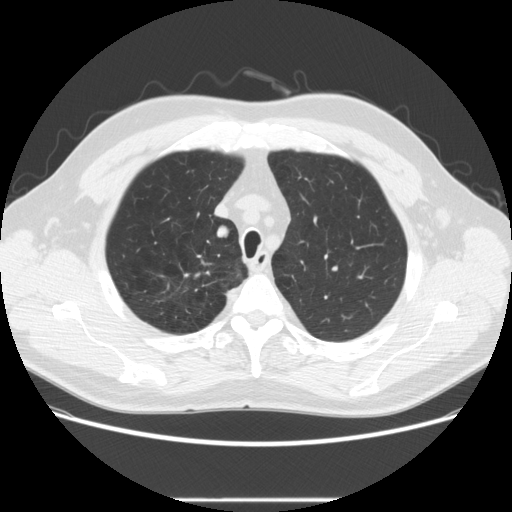
Low-dose screening chest CT, axial slice; baseline screening round; lung window (W 1500 / L -600 HU); 2.5 mm slice thickness. Male participant, aged 64 years at enrolment. Former smoker at enrolment.
Lesion marked by an expert reader, bounding box [x1, y1, x2, y2] px = [196, 220, 239, 252]. The screening reader recorded 2 non-calcified nodules or masses ≥4 mm on this exam (right upper lobe, right upper lobe); which of them this box marks is not recorded. Official screen result: positive, change unspecified: nodule(s) >= 4 mm or enlarging nodule(s), mass(es), or other non-specific abnormalities suspicious for lung cancer. Participant outcome: lung cancer diagnosed 753 days after this screen — adenocarcinoma, NOS, right upper lobe, moderately differentiated (G2), stage IA (AJCC 6th edition), 14 mm at pathology.